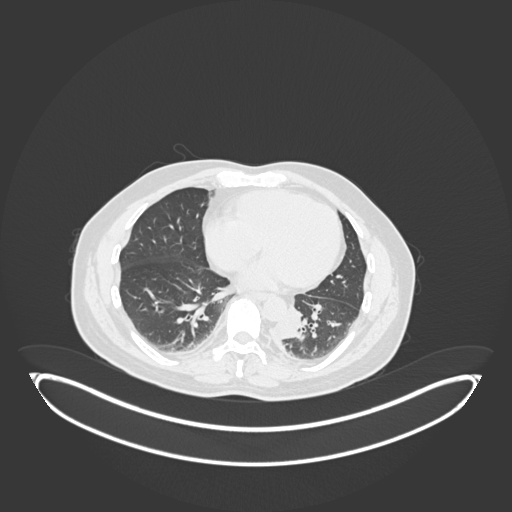
Chest CT, one axial slice. Position 64 of 258 along the scan axis. Reconstruction kernel B30f. Lung window (W 1500 / L -600 HU). 512 × 512 image matrix, field of view 500 × 500 mm. Male patient, age 54 years. From the clinical record (not read from this slice): clinical TNM (as recorded): T3 N0 M0.
Annotated regions visible in this slice (rectangle marked by the reading radiologist):
- lung tumour (recorded histology: squamous cell carcinoma): bounding box (x1, y1, x2, y2) in pixels: (275, 306, 314, 346)